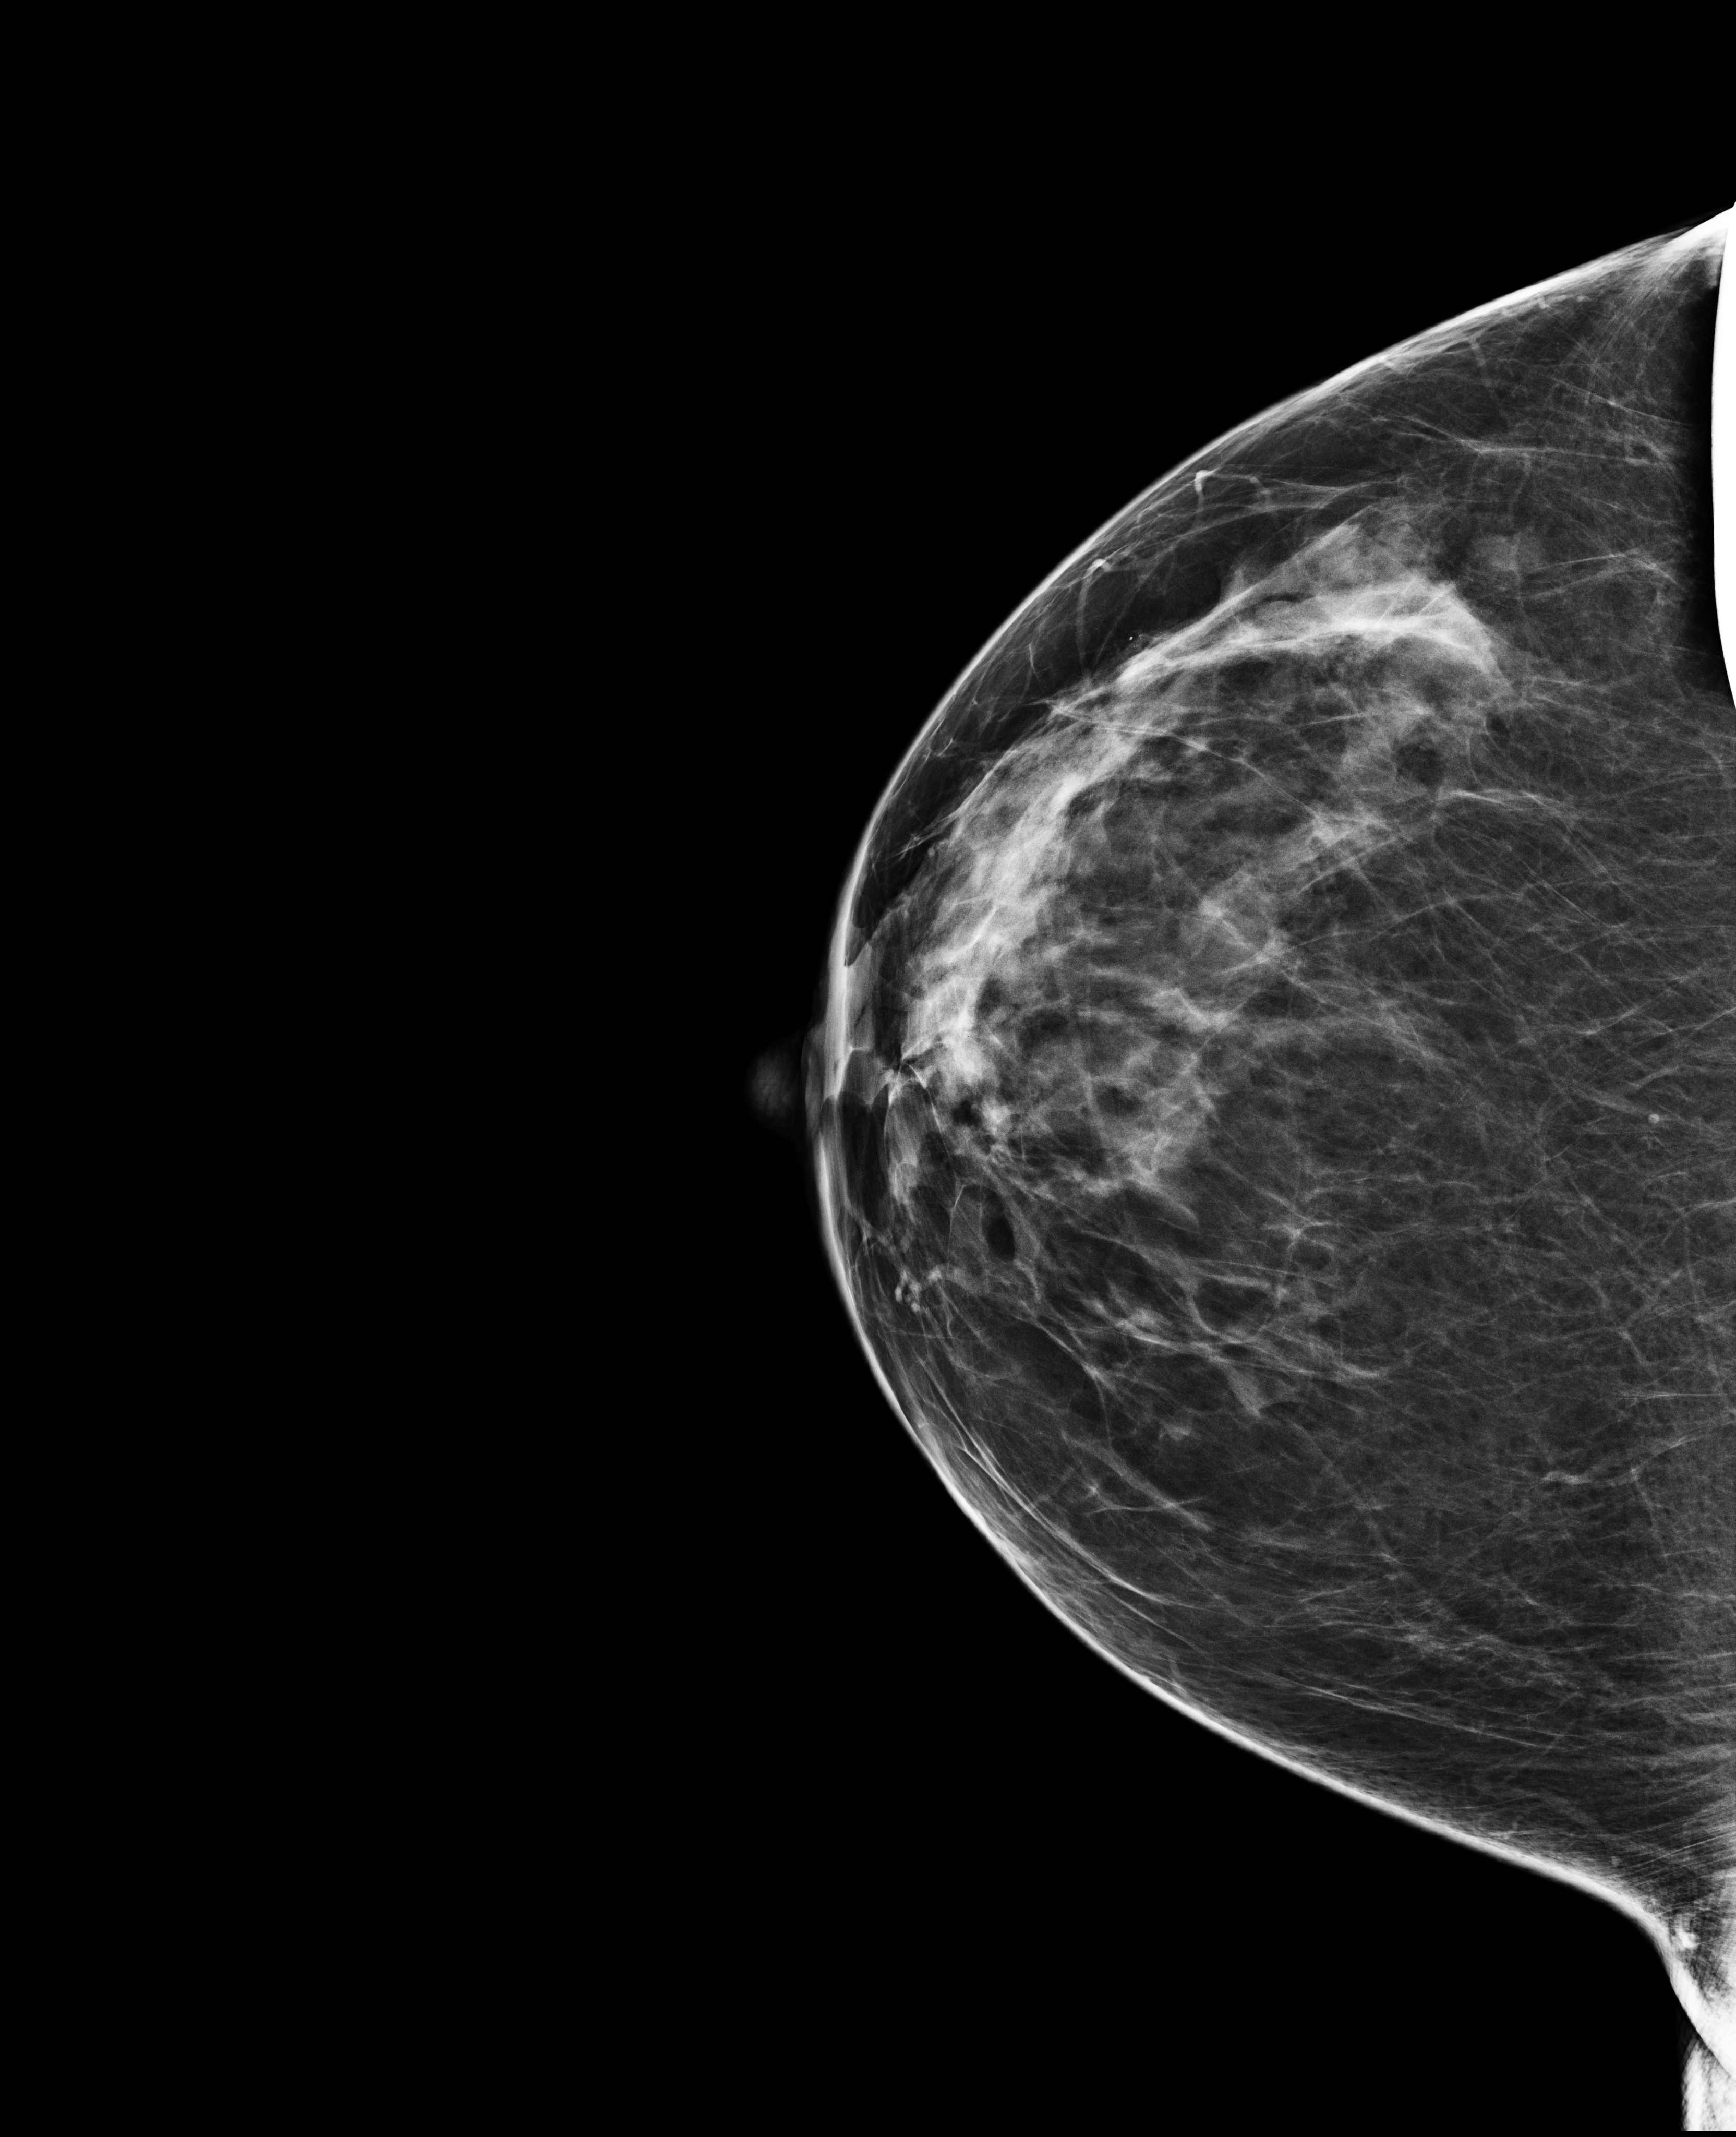
Digital mammogram (FFDM), right breast, craniocaudal (CC) view, annual screening mammography examination. Patient aged 57 years (female).
BI-RADS breast density category at the screening exam (both breasts, scale 1–4): 3. Final BI-RADS assessment for this screening round (tomosynthesis exam, both breasts): category 1. Recall: no recall after this screen.